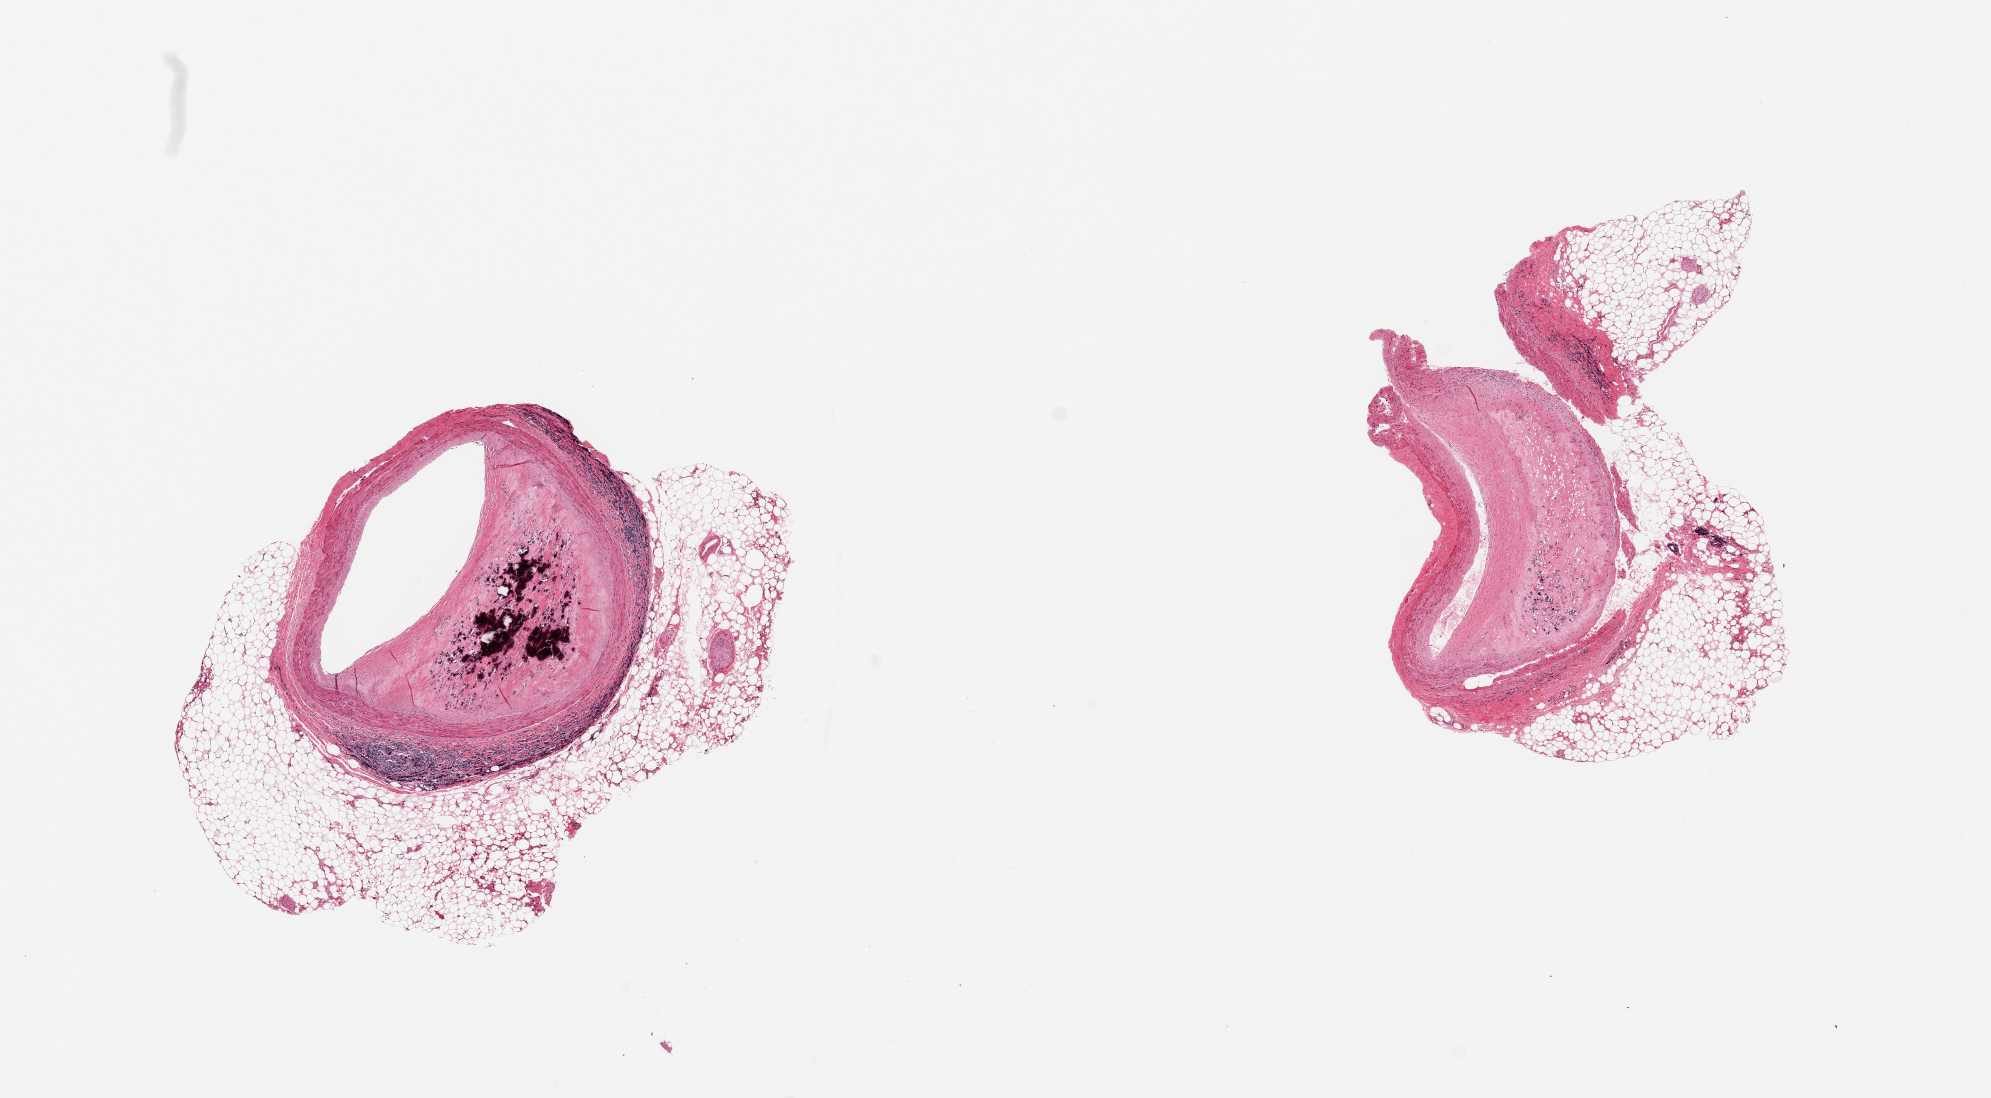
Whole-slide image, haematoxylin and eosin stain, low-resolution overview of the scanned area, about 15.8 x 8.7 mm (from a 20x scan), PAXgene-fixed paraffin-embedded (PFPE) section, target tissue: coronary artery, donor tissue sample. Male donor.
• pathologist's review note for this sample: 2 pieces, ~70-80% occlusive calcified atherosis, adherent fat up to ~1.5mm